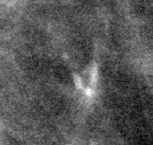
Crop from a digitized film mammogram around one marked abnormality, left breast, MLO view, BI-RADS breast density category 2 (scale 1–4).
- Calcifications, morphology fine linear branching, distribution clustered / linear; BI-RADS assessment category 4; subtlety rating 3 on a 1 (subtle) to 5 (obvious) scale; pathology (as recorded): malignant.